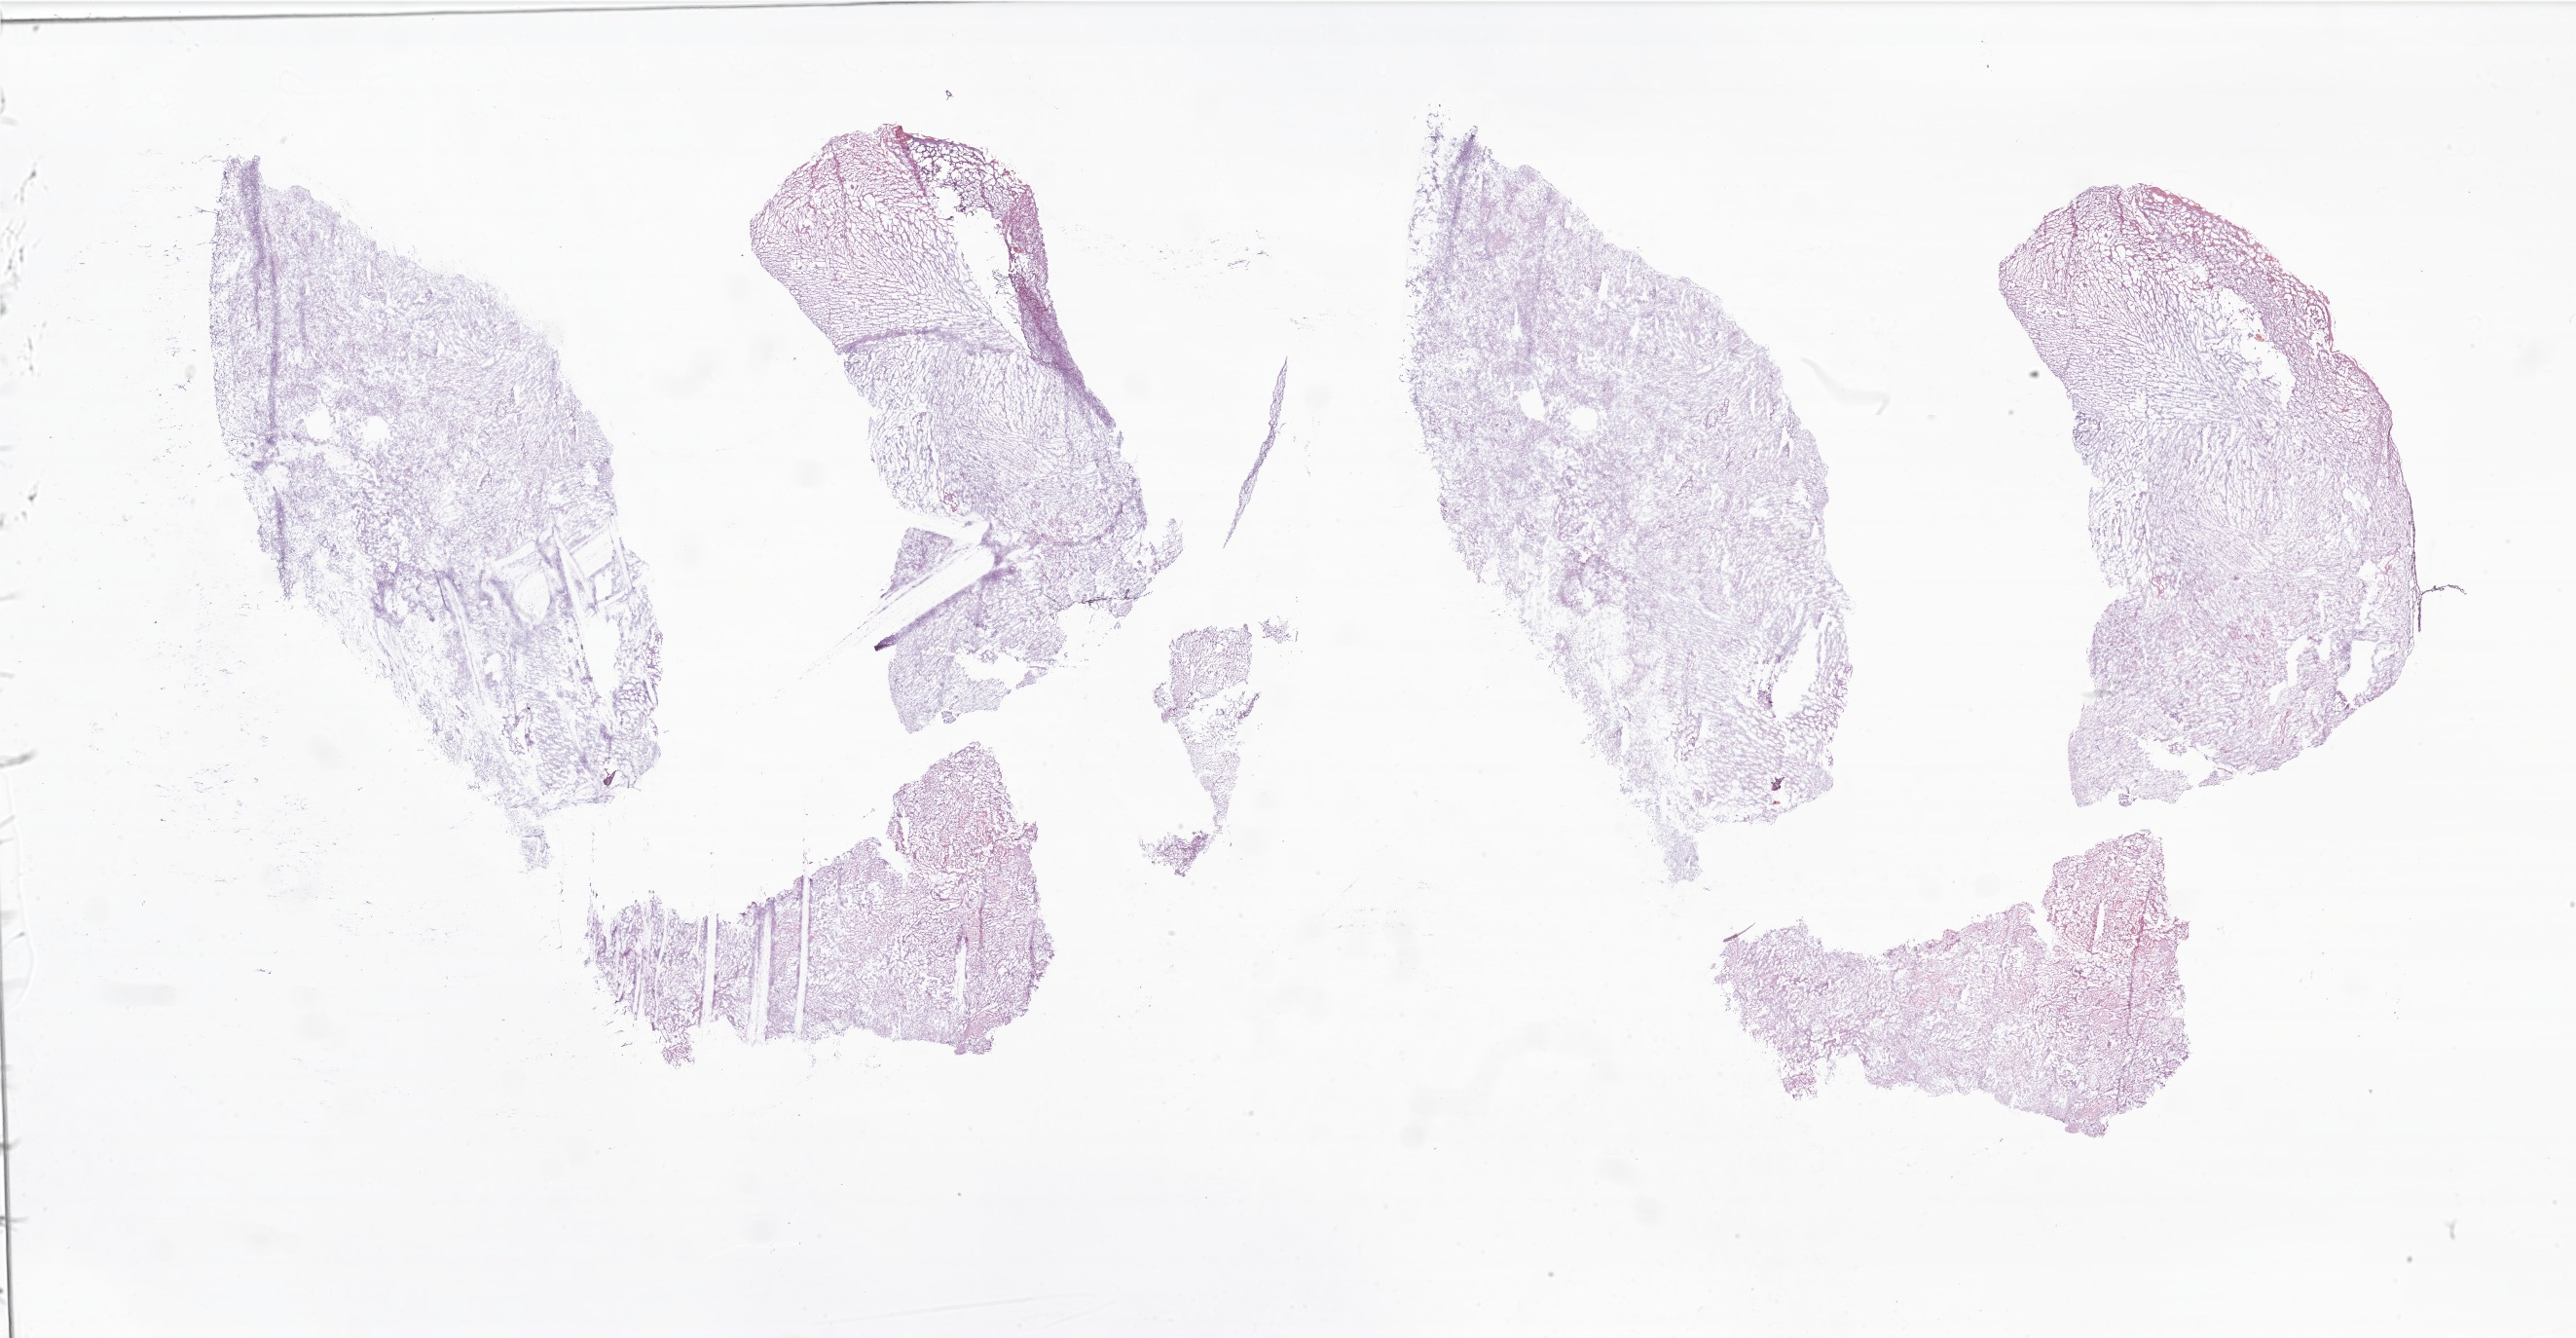
Digitized haematoxylin and eosin-stained section of tumor tissue from the cerebellum, whole scanned area (about 44.6 x 23.2 mm) shown as a low-resolution overview; frozen section. Patient: female, age 57 months (4 years 9 months).
• diagnosis: Pilocytic astrocytoma